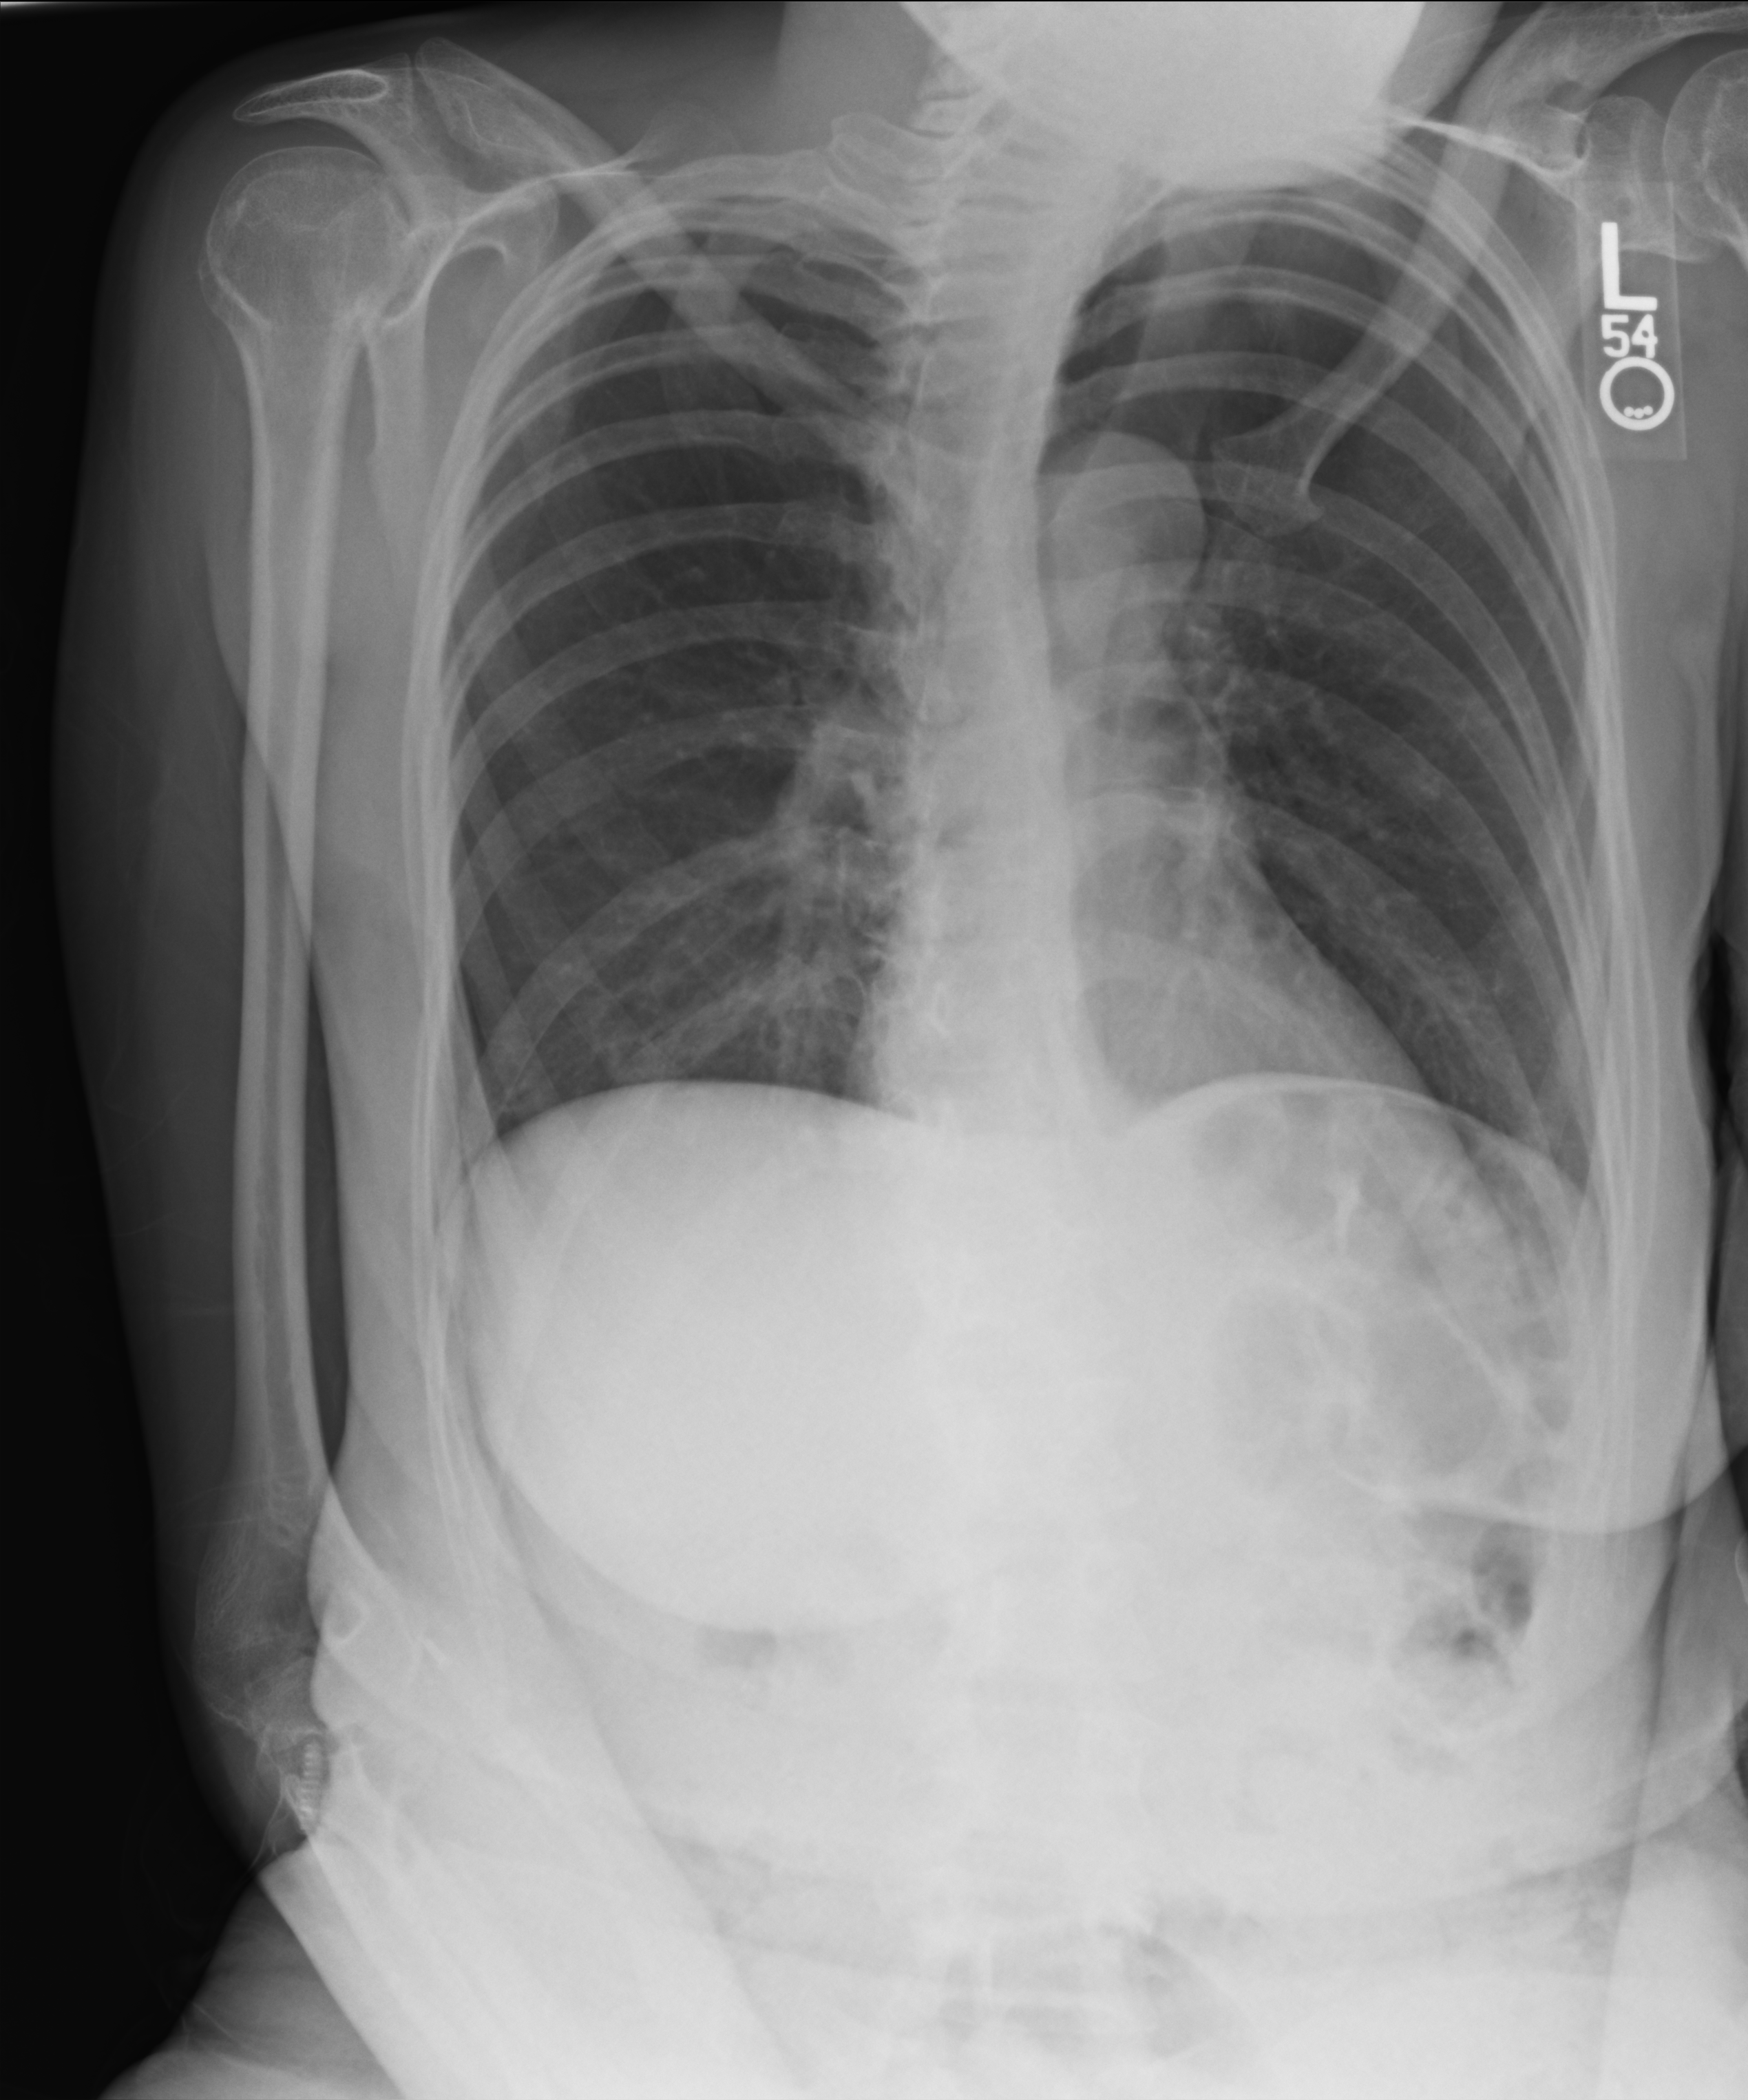
Portable chest radiograph. Female patient hospitalised with COVID-19, age 18–59 years.
Admission-level facts for this patient (not findings on this image; timing relative to this image not recorded): chronic kidney disease (admission record): no.